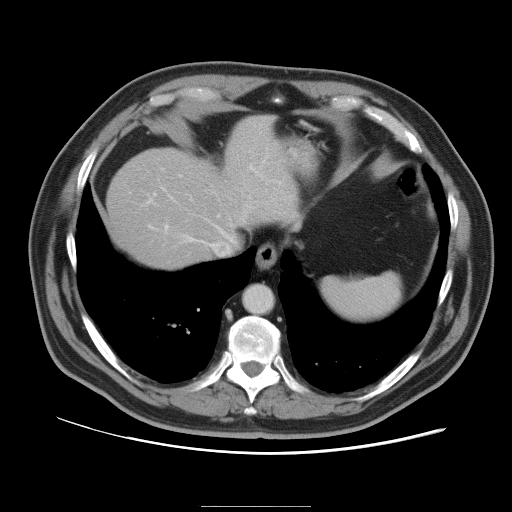
Contrast-enhanced abdominal CT, one axial slice; slice 85 of 105 in the series (ordered by position); intravenous contrast given; soft-tissue window (W 400 / L 40 HU); 5 mm slice thickness; 512 × 512 image matrix. Male patient, age 64 years. Case-level facts recorded for this patient, not image findings: diagnosis: colorectal cancer liver metastases, imaged before liver resection; multiple liver metastases: yes; largest metastasis: 3 cm; disease in both lobes: yes.
Structures marked on this image (outlined manually by an expert reader):
- hepatic veins: bounding box <148,194,250,241> (left, top, right, bottom; pixels)
- liver: <107,115,296,268>
- planned liver remnant (the part of the liver to remain after resection): <107,154,231,268>
- portal vein (with intrahepatic branches): <146,167,252,234>